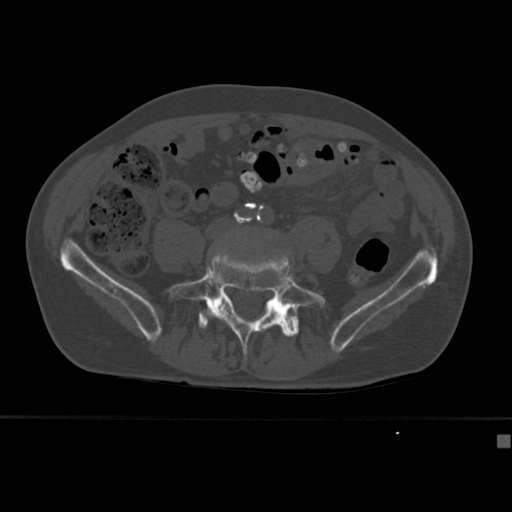
CT including the spine, one axial slice. Position 89 of 430 along the scan axis. Reconstruction kernel Br40s. 120 kVp. Bone window (W 1800 / L 400 HU). 1.5 mm slice thickness. 512 × 512 image matrix. Patient: male, 64 years. Case-level facts recorded for this patient, not image findings: primary cancer: uterus.
Annotated regions visible in this slice (semi-automatic segmentation, software-assisted and operator-edited):
- L5 vertebra: box from (x=168, y=249) to (x=327, y=362) px